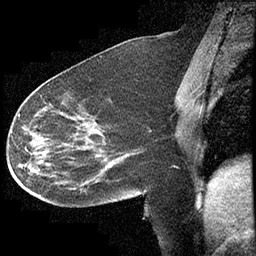
Breast MRI (dynamic contrast-enhanced), one sagittal slice; position 171 of 232 along the scan axis; dynamic contrast-enhanced study with each time point stored as its own series, time point 2 of 4 at this slice position (early post-contrast, ordered by acquisition time); 1.5 T; TE 4.2 ms, TR 6.7 ms; 3 mm slice thickness; 256 × 256 image matrix, field of view 200 × 200 mm. Patient: female, 63 years. Case-level facts recorded for this patient, not image findings: setting: breast cancer imaged before/during neoadjuvant chemotherapy; receptor status: triple-negative.
Outlined on this slice (semi-automatic segmentation, software-assisted and operator-edited):
- analysis volume of interest (the breast-tissue region the enhancement analysis was run in; not a lesion): bounding box <13,90,140,208> (left, top, right, bottom; pixels)
- tumour enhancement mask (voxels above the 70 % enhancement threshold inside the analysis volume of interest): <19,114,79,151>